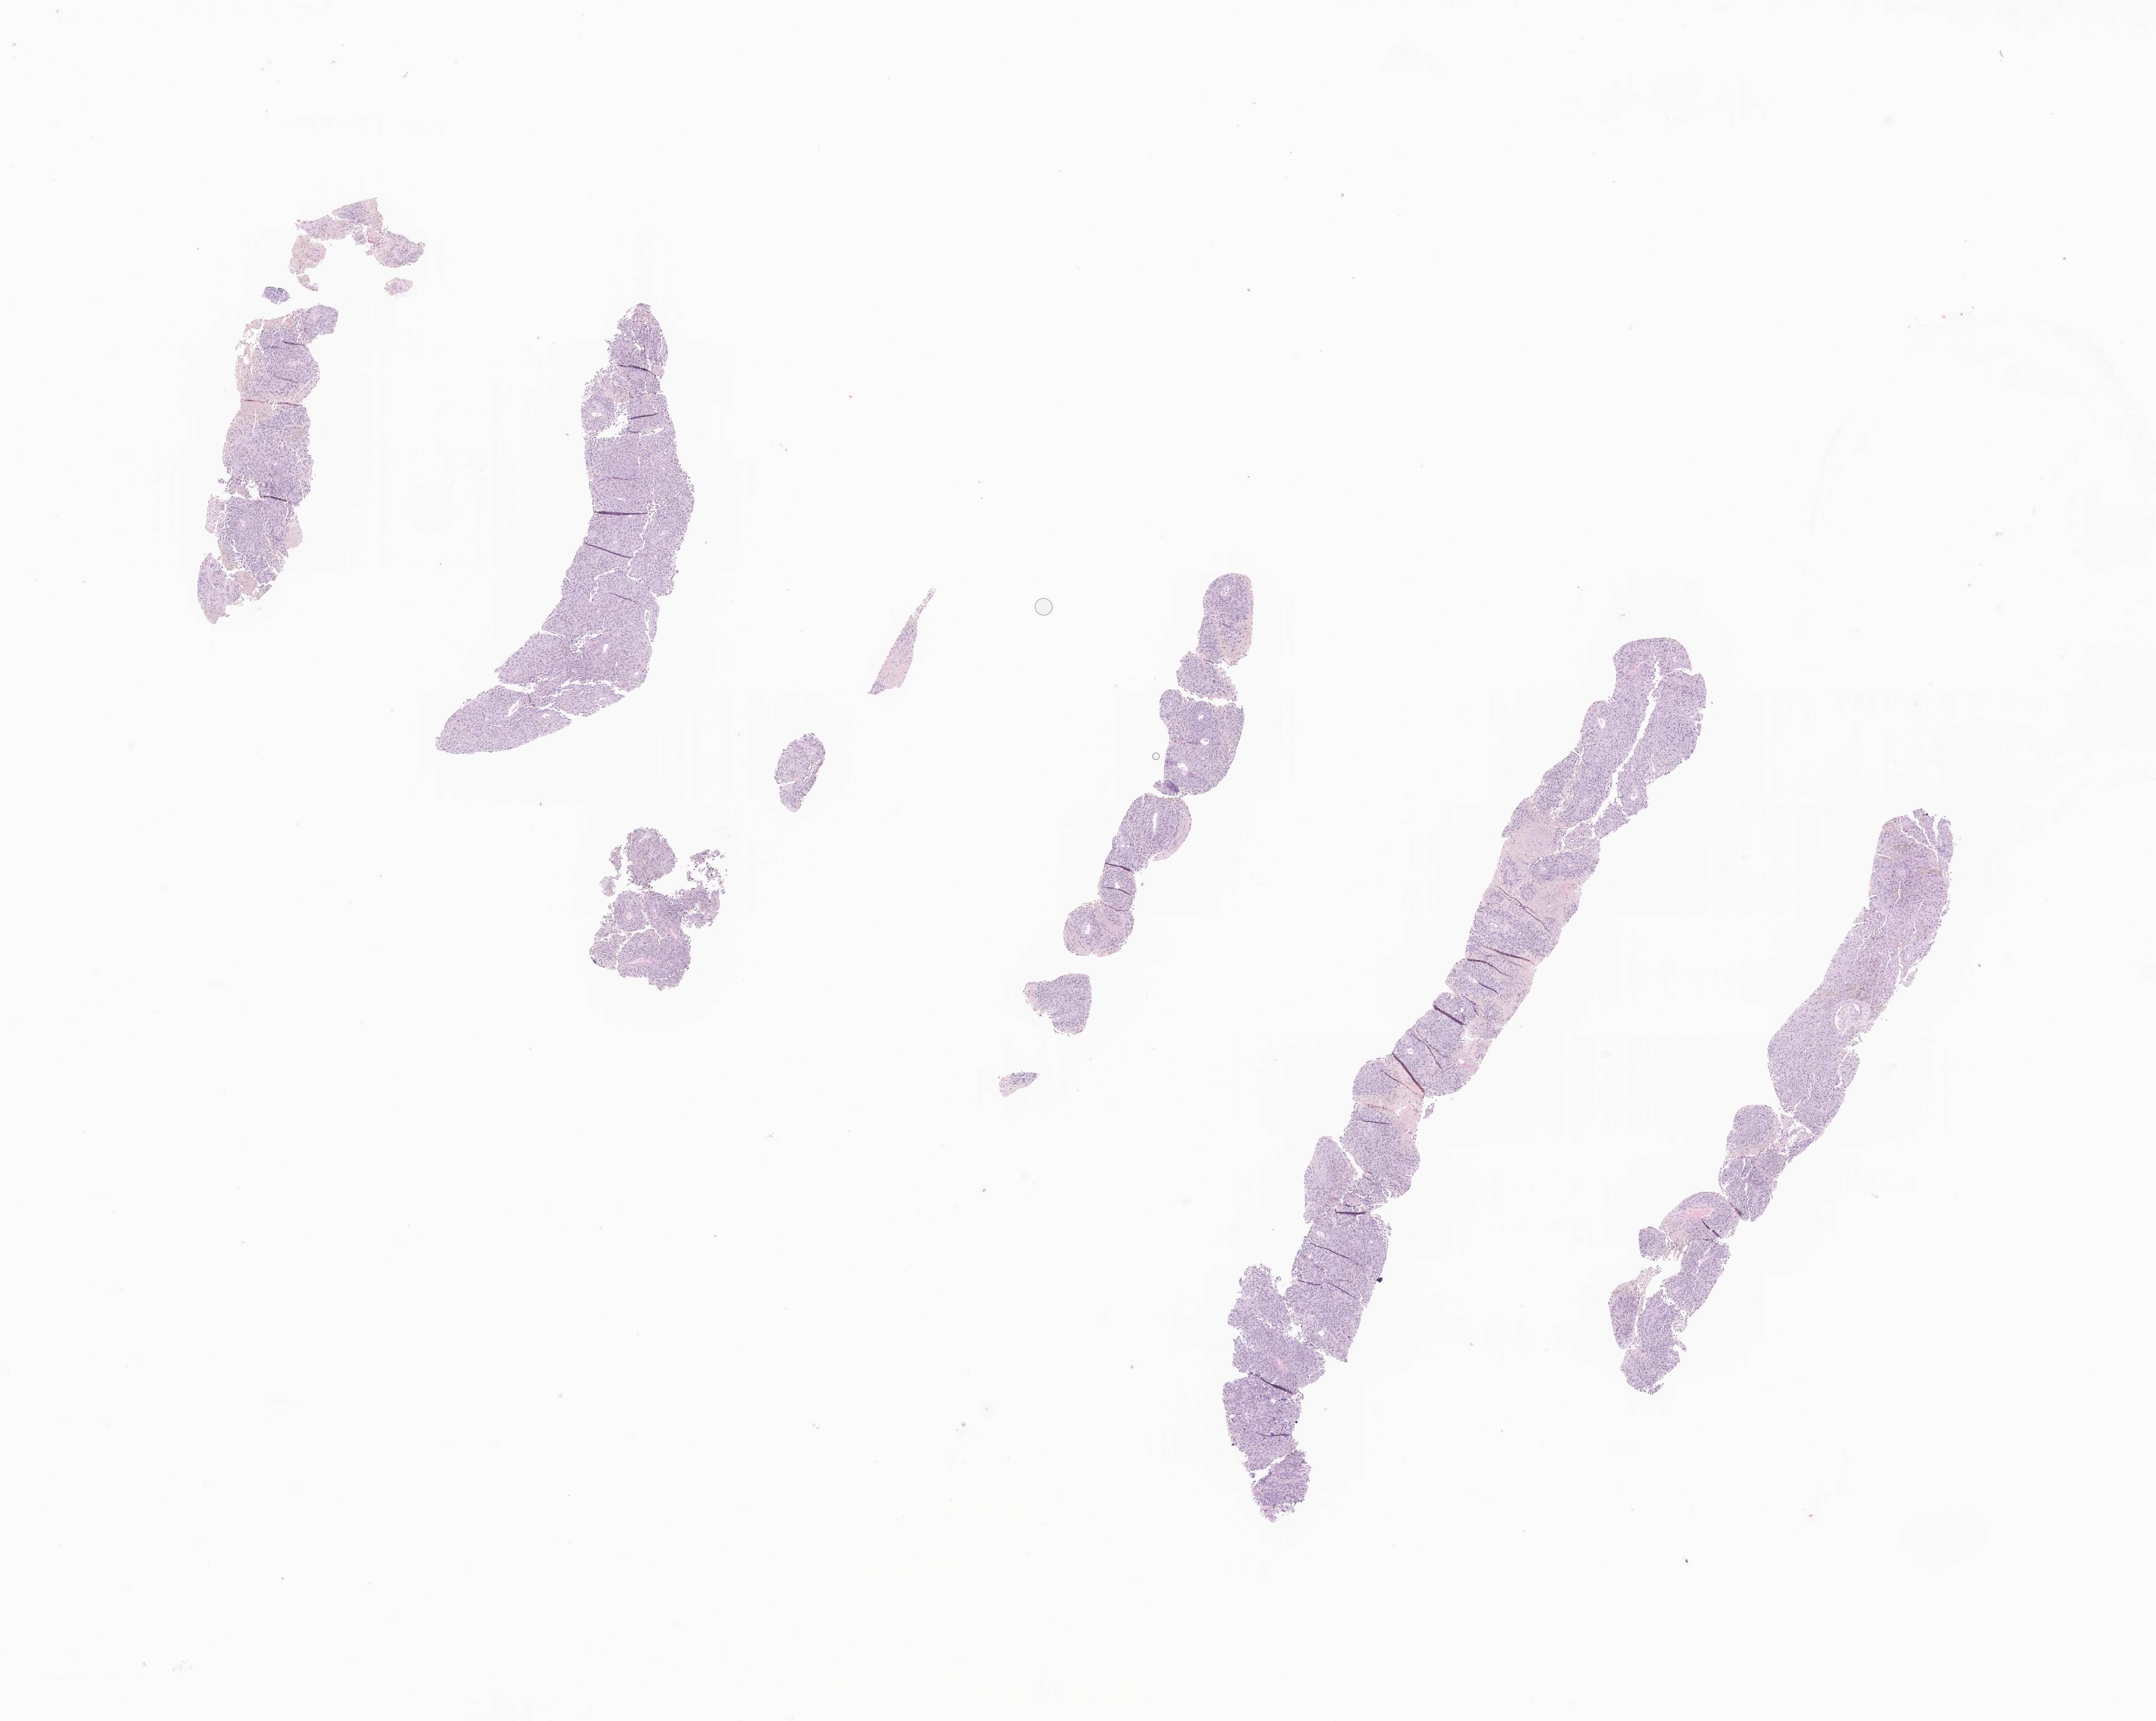
Whole-slide image, hematoxylin and eosin (H&E) stain of tumor tissue from the soft tissue of lower extremity, low-resolution overview of the scanned area, about 20.0 x 16.0 mm, FFPE section. Patient: female, age 189 months (15 years 9 months).
Recorded diagnosis: Malignant melanoma, NOS.